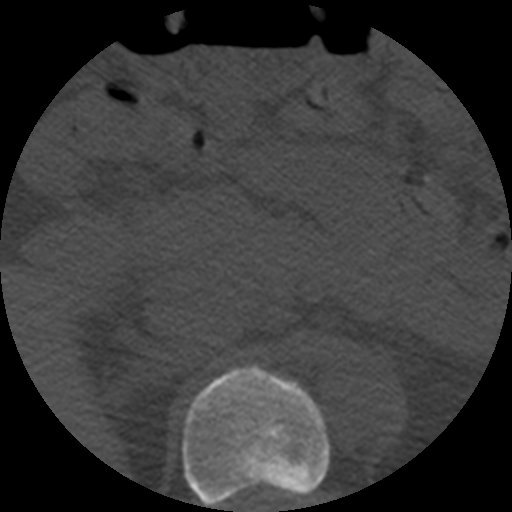
CT including the spine, one axial slice. Slice 234 of 508 in the series (ordered by position). Reconstruction kernel STANDARD. 120 kVp. Bone window (W 1800 / L 400 HU). 1.25 mm slice thickness. 512 × 512 image matrix, field of view 160 × 160 mm. Patient age 57 years. From the clinical record (not read from this slice): primary cancer: prostate.
Outlined on this slice (semi-automatic segmentation, software-assisted and operator-edited):
- T11 vertebra: bounding box [x1, y1, x2, y2] px = [182, 366, 330, 507]